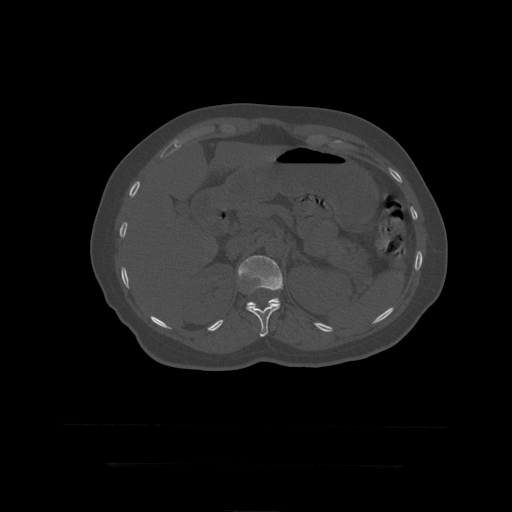
CT including the spine, one axial slice; position 188 of 399 along the scan axis; bone window (W 1800 / L 400 HU); 1.25 mm slice thickness; 512 × 512 image matrix, field of view 450 × 450 mm. Patient age 41 years. From the clinical record (not read from this slice): primary cancer: breast.
Annotated regions visible in this slice (semi-automatic segmentation, software-assisted and operator-edited):
- L1 vertebra: box from (x=238, y=256) to (x=284, y=309) px
- T12 vertebra: (x=247, y=289)–(x=281, y=337)